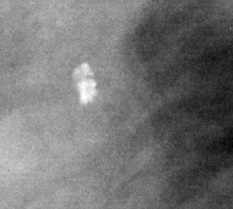
Cropped region of a digitized screen-film mammogram centred on a radiologist-marked abnormality, right breast, MLO view, BI-RADS breast density category 3 (scale 1–4).
- Marked abnormality: calcifications, morphology lucent center; BI-RADS assessment category 2; benign without callback (not worked up further).